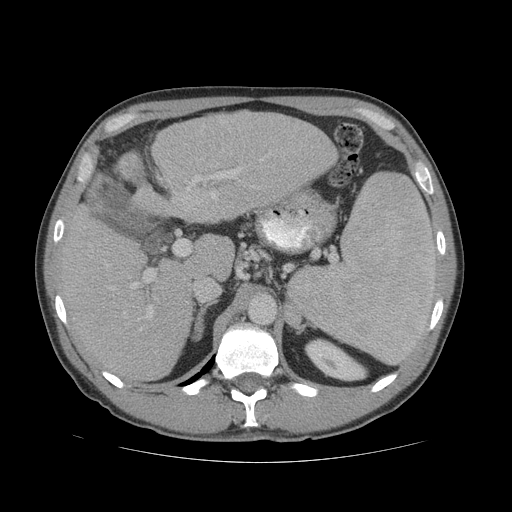
Contrast-enhanced abdominal CT (liver protocol), one axial slice; position 39 of 81 along the scan axis; reconstruction kernel STANDARD; soft-tissue window (W 400 / L 40 HU); 512 × 512 image matrix, field of view 400 × 400 mm. Case-level facts recorded for this patient, not image findings: diagnosis: hepatocellular carcinoma (patient treated with transarterial chemoembolisation; whether this scan precedes or follows treatment is not stated here); TNM stage (as recorded): Stage-IVB; Child-Pugh class: B; tumour differentiation: well differentiated; tumour nodularity: multinodular.
Annotated regions visible in this slice (semi-automatically segmented with operator editing):
- liver parenchyma outside the tumour (the mass and vessels are separate outlines, so this box may not span the whole liver): bounding box [x1, y1, x2, y2] px = [54, 110, 338, 382]
- liver vessels: [106, 152, 271, 318]